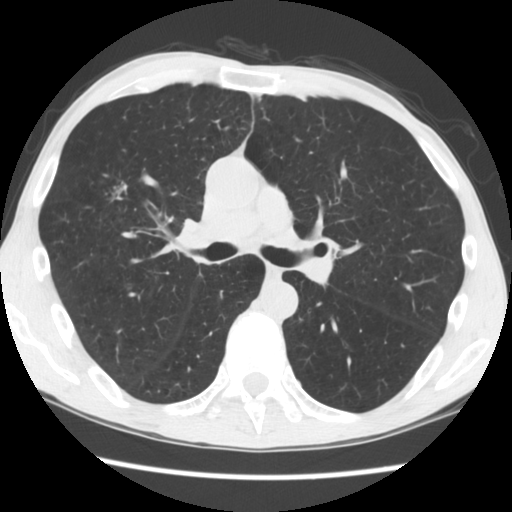
Low-dose screening chest CT, axial slice. Second annual screen. Lung window (W 1500 / L -600 HU). 2.5 mm slice thickness. Standard (soft-tissue) reconstruction kernel (STANDARD). 512 × 512 image matrix. Male, age 56 years at enrolment. Current smoker at enrolment.
Lesion marked by an expert reader, bounding box <93,176,147,231> (left, top, right, bottom; pixels). The screening reader recorded 2 non-calcified nodules or masses ≥4 mm on this exam (right upper lobe, left upper lobe); which of them this box marks is not recorded. Official screen result: positive, change unspecified: nodule(s) >= 4 mm or enlarging nodule(s), mass(es), or other non-specific abnormalities suspicious for lung cancer.